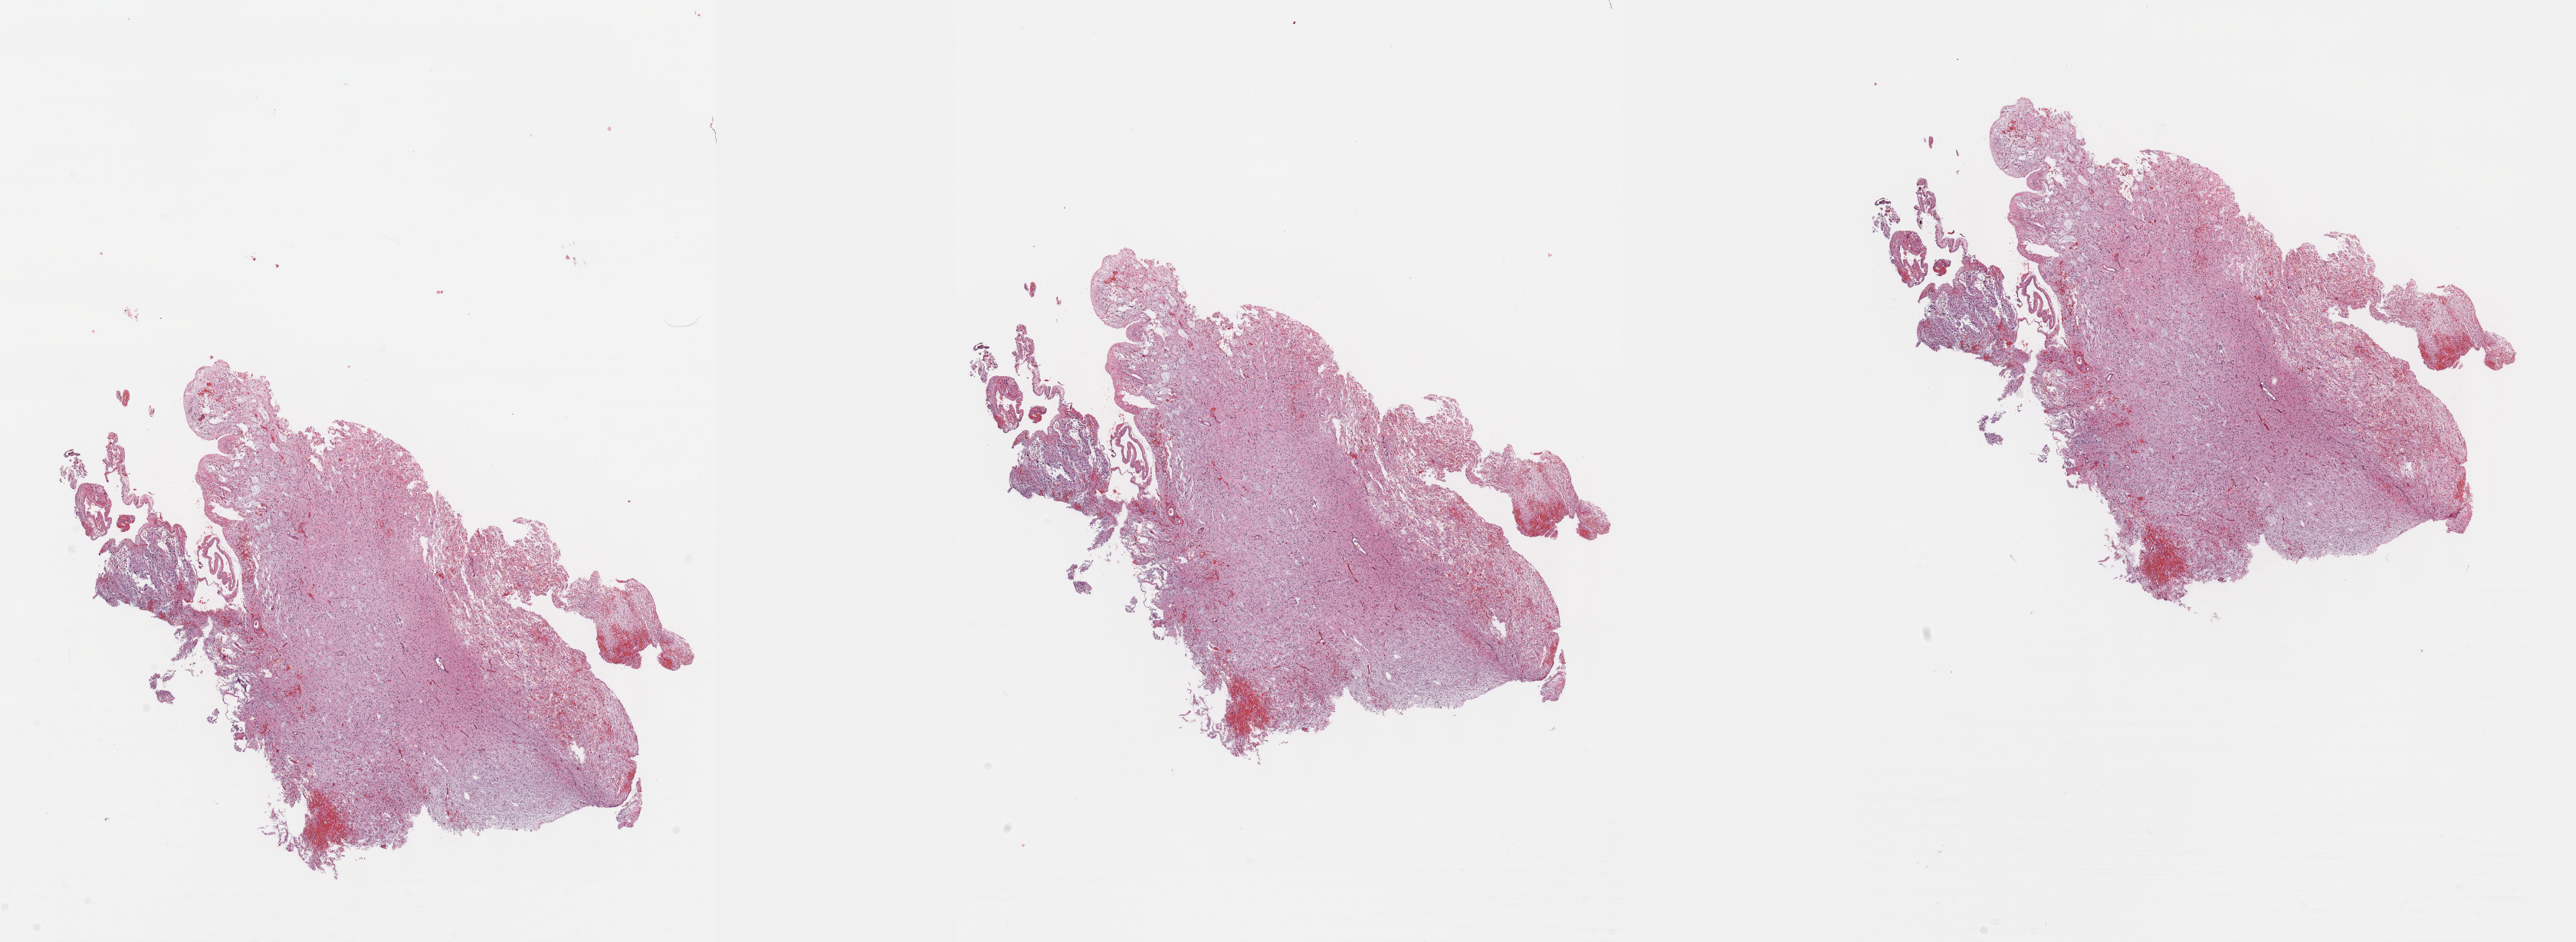
Digitized H&E tissue section (whole slide), low-resolution overview of the scanned area, about 27.2 x 9.9 mm (acquisition: 40x scan); formalin-fixed paraffin-embedded (FFPE) diagnostic section; brain, primary tumour sample. Male patient; age at initial diagnosis 43 years. Histologic grade: G3 (poorly differentiated).
Pathologic diagnosis: Mixed glioma. Laterality: left.